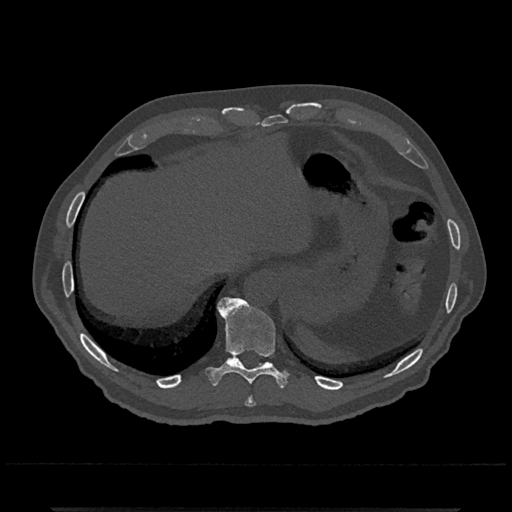
CT including the spine, one axial slice; slice 551 of 797 in the series (ordered by position); bone window (W 1800 / L 400 HU); 0.5 mm slice thickness; 512 × 512 image matrix, field of view 393 × 393 mm. Patient: male, 67 years. Case-level facts recorded for this patient, not image findings: primary cancer: prostate.
Annotated regions visible in this slice (semi-automatically segmented with operator editing):
- T10 vertebra: bounding box [x1, y1, x2, y2] px = [206, 297, 287, 388]
- T11 vertebra: [228, 357, 239, 361]
- T9 vertebra: [245, 396, 256, 407]